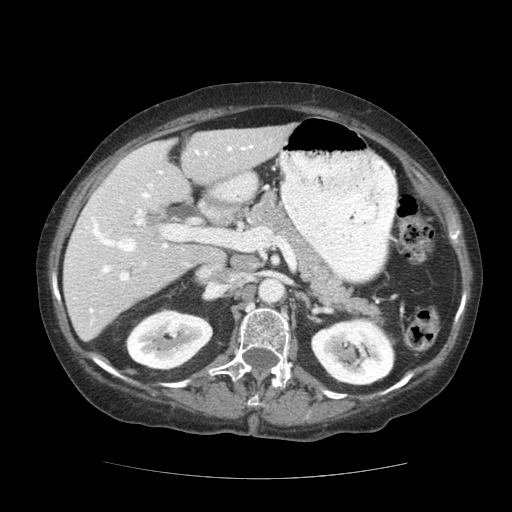
Contrast-enhanced abdominal CT (liver protocol), one axial slice; slice 68 of 111 in the series (ordered by position); reconstruction kernel STANDARD; 140 kVp; soft-tissue window (W 400 / L 40 HU); 2.5 mm slice thickness; 512 × 512 image matrix, field of view 360 × 360 mm. From the clinical record (not read from this slice): diagnosis: hepatocellular carcinoma (patient treated with transarterial chemoembolisation; whether this scan precedes or follows treatment is not stated here); TNM stage (as recorded): Stage-I.
Annotated regions visible in this slice (semi-automatic segmentation, software-assisted and operator-edited):
- liver parenchyma outside the tumour (the mass and vessels are separate outlines, so this box may not span the whole liver): bounding box [x1, y1, x2, y2] px = [64, 124, 292, 340]
- liver vessels: [78, 144, 253, 325]